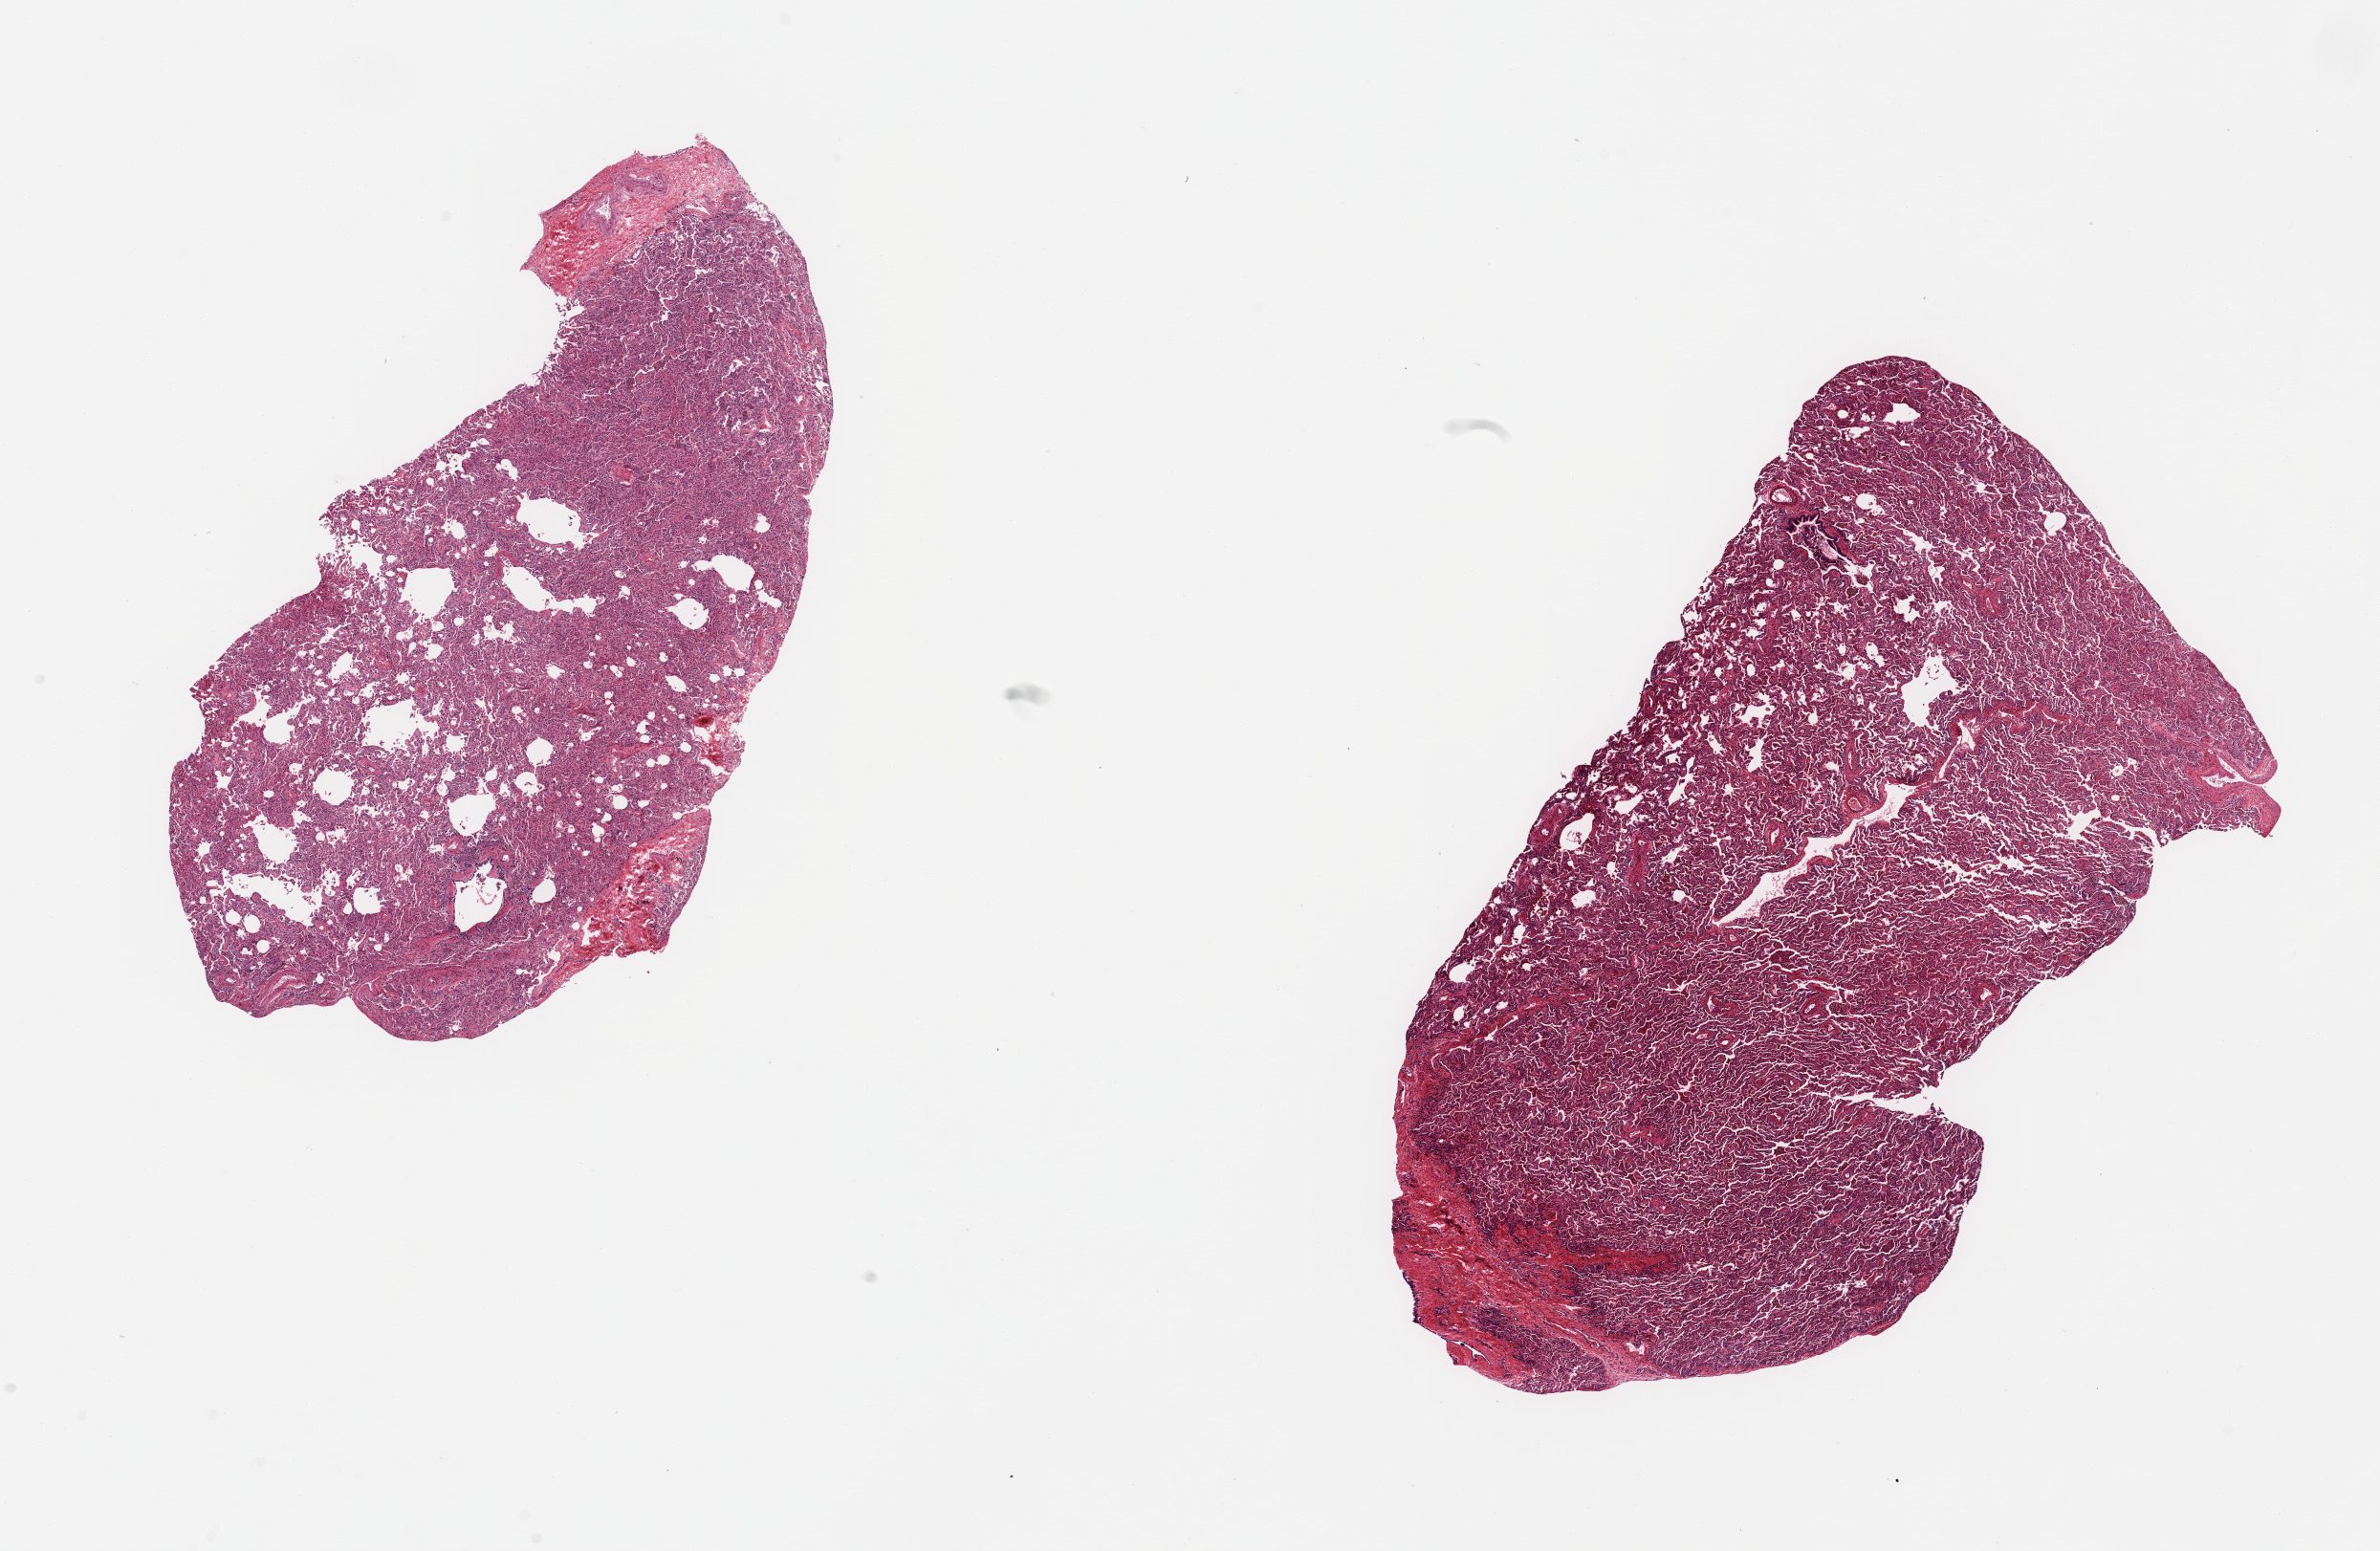
Haematoxylin and eosin whole-slide image, shown as a low-resolution overview of the whole scanned area (about 19.7 x 12.8 mm, acquisition: 20x scan), PAXgene-fixed, paraffin-embedded tissue, sampled site (target tissue): lung, tissue donor sample.
Reviewer comment on this tissue sample: 2 pieces; atelectatic (?procedural); 1.5mm2 fibrovascular focus at one edge.